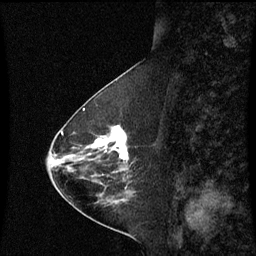
Breast MRI (dynamic contrast-enhanced), one sagittal slice. Slice 25 of 60 in the series (ordered by position). Dynamic contrast-enhanced series, image 2 of 3 at this slice position (ordered by acquisition). 1.5 T. TE 4.2 ms, TR 8.9 ms. 2 mm slice thickness. 256 × 256 image matrix. Patient: female, 63 years. From the clinical record (not read from this slice): setting: breast cancer imaged before/during neoadjuvant chemotherapy; receptor status: HR-positive, HER2-negative.
Annotated regions visible in this slice (semi-automatically segmented with operator editing):
- analysis volume of interest (the breast-tissue region the enhancement analysis was run in; not a lesion): bounding box <94,126,134,177> (left, top, right, bottom; pixels)
- tumour enhancement mask (voxels above the 70 % enhancement threshold inside the analysis volume of interest): <95,126,129,161>